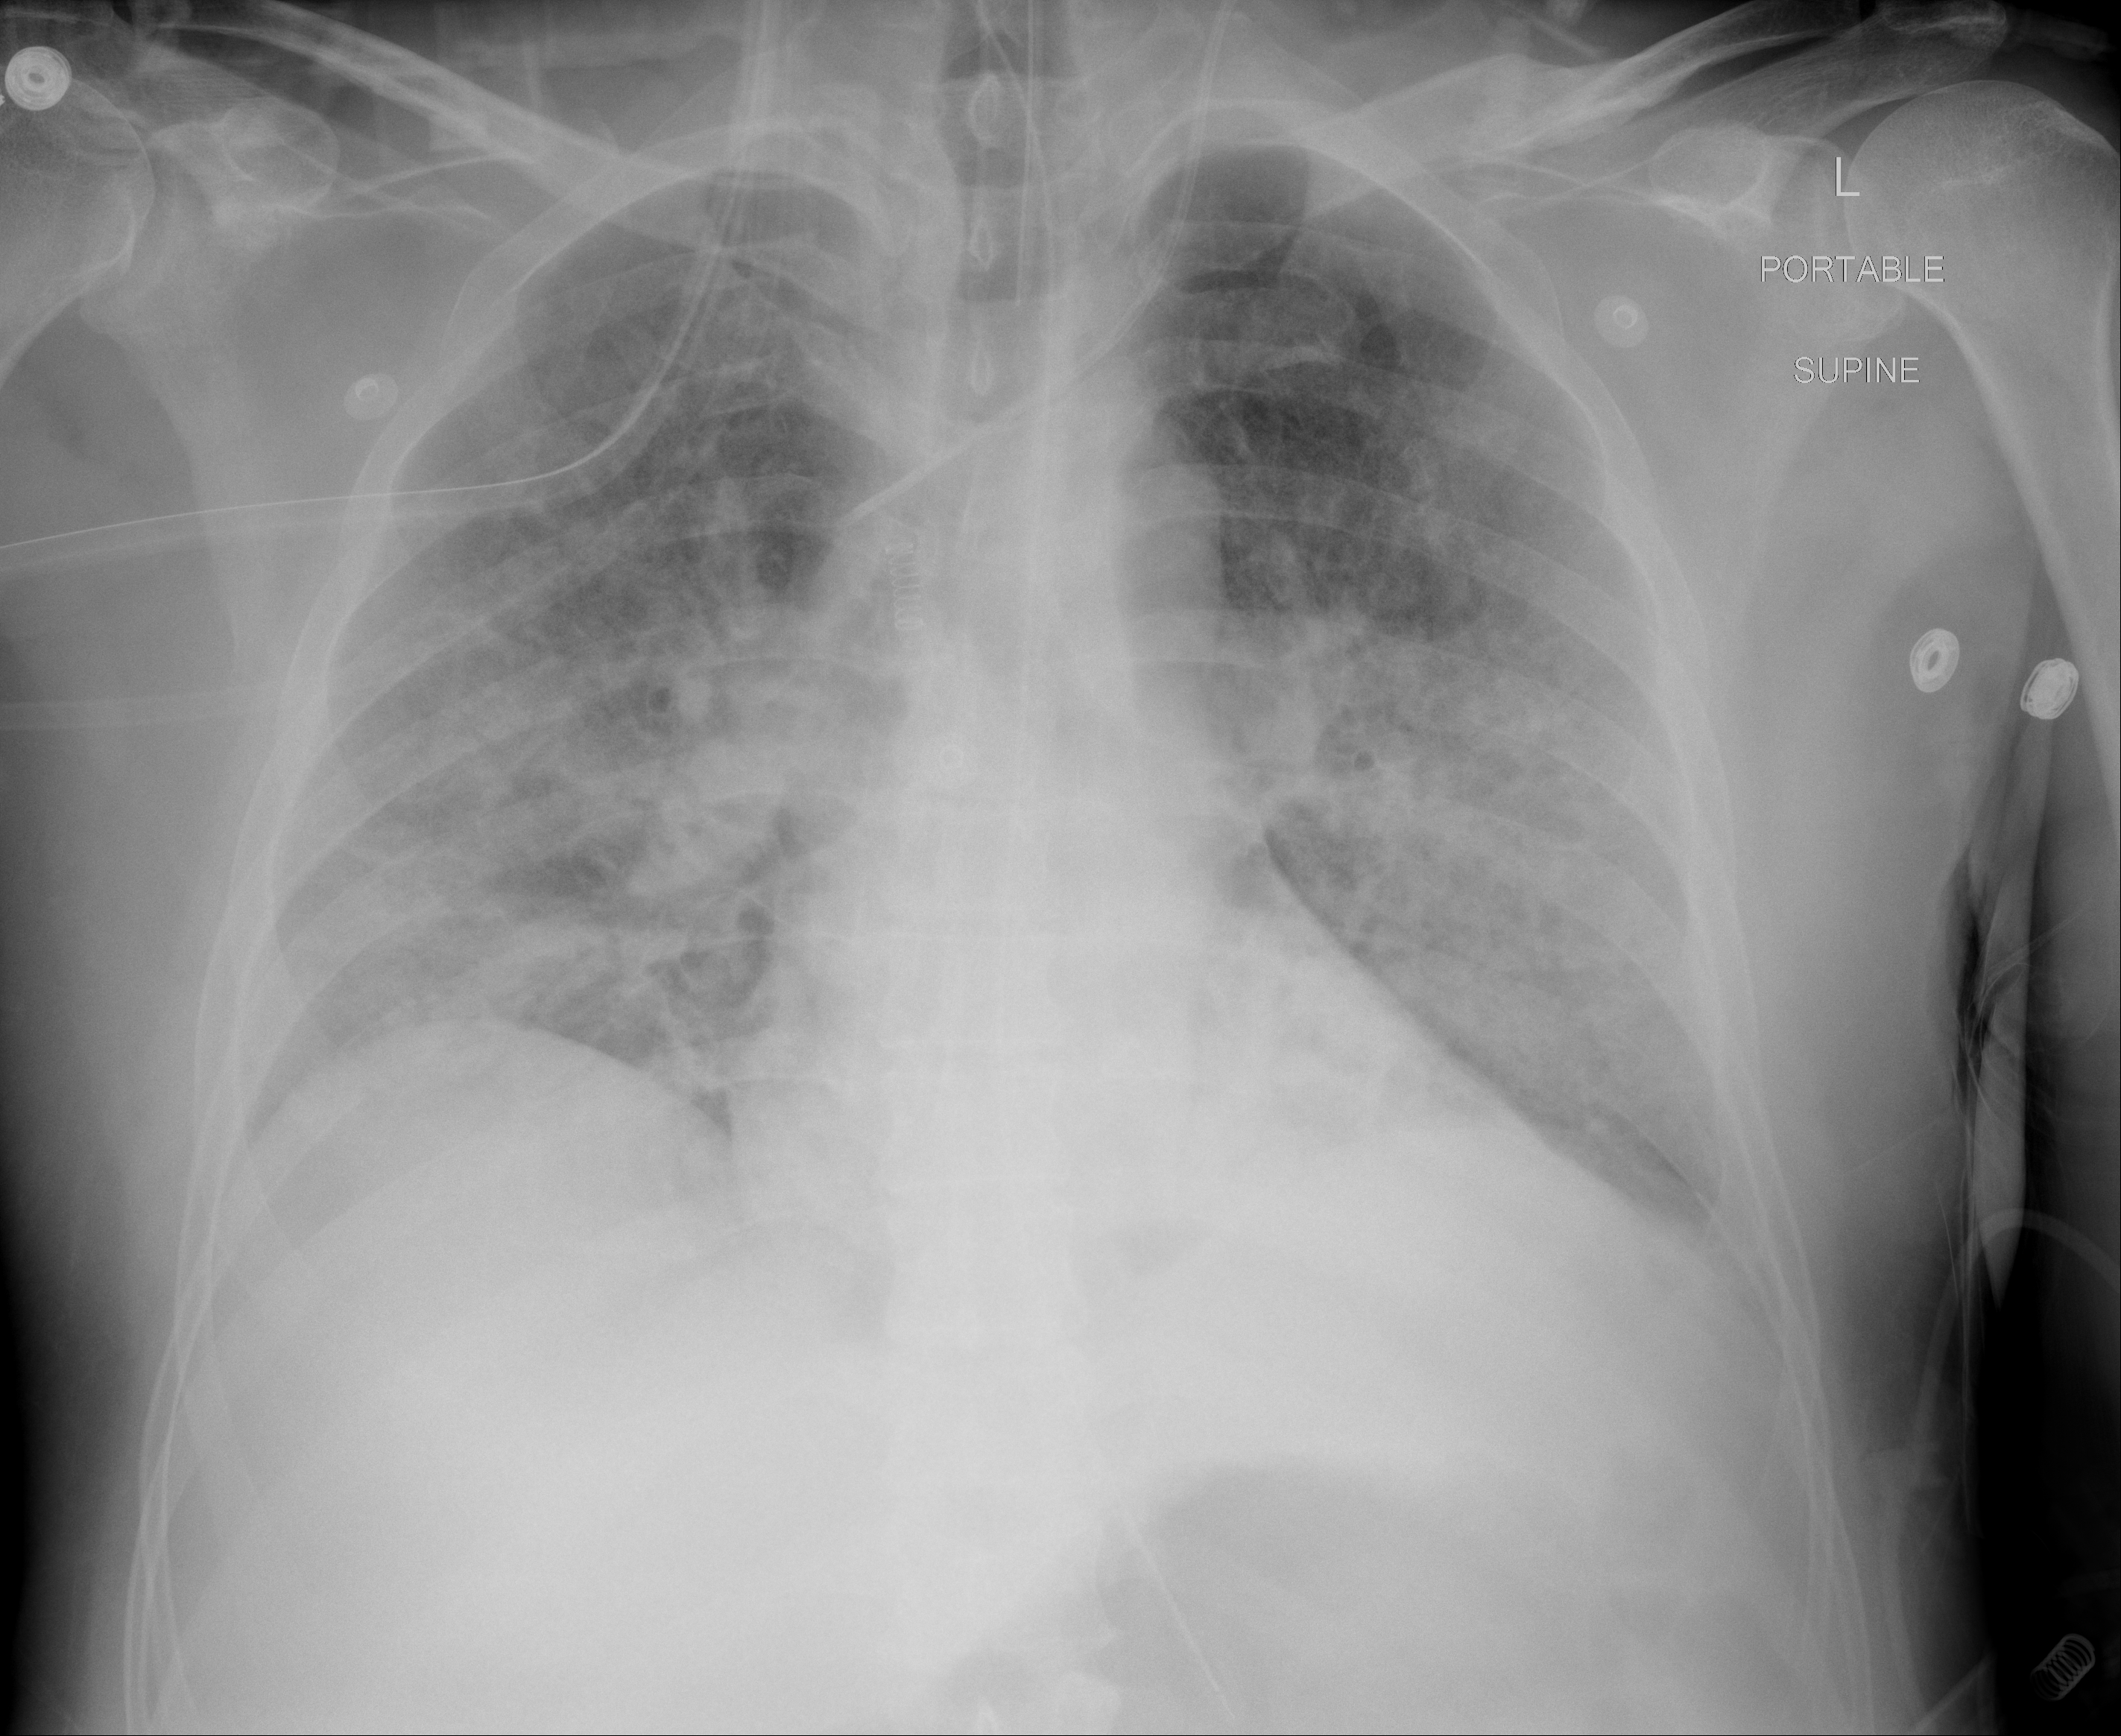
Chest X-ray (portable), AP projection. Male patient, age 57 years; imaged 1 day after the COVID-19 diagnosis.
Radiologist key findings (as recorded): Interval worsening airspace opacities in both lungs. Mild bilateral pleural effusions.